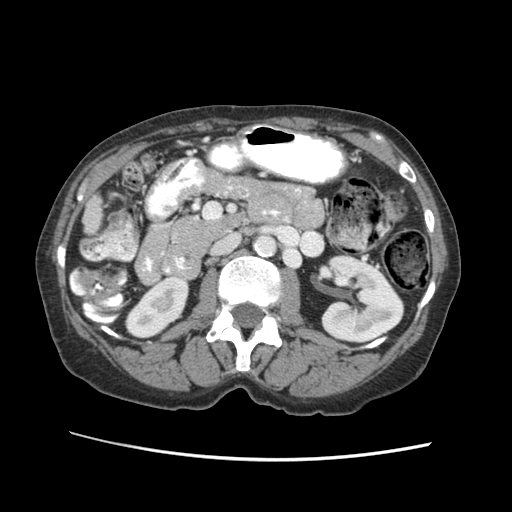
Contrast-enhanced abdominal CT (liver protocol), one axial slice. Position 7 of 63 along the scan axis. 120 kVp. Soft-tissue window (W 400 / L 40 HU). 512 × 512 image matrix. Case-level facts recorded for this patient, not image findings: diagnosis: hepatocellular carcinoma (patient treated with transarterial chemoembolisation; whether this scan precedes or follows treatment is not stated here); TNM stage (as recorded): Stage-I; Child-Pugh class: B; tumour nodularity: uninodular.
Annotated regions visible in this slice (semi-automatic segmentation, software-assisted and operator-edited):
- liver parenchyma outside the tumour (the mass and vessels are separate outlines, so this box may not span the whole liver): box from (x=84, y=192) to (x=106, y=248) px